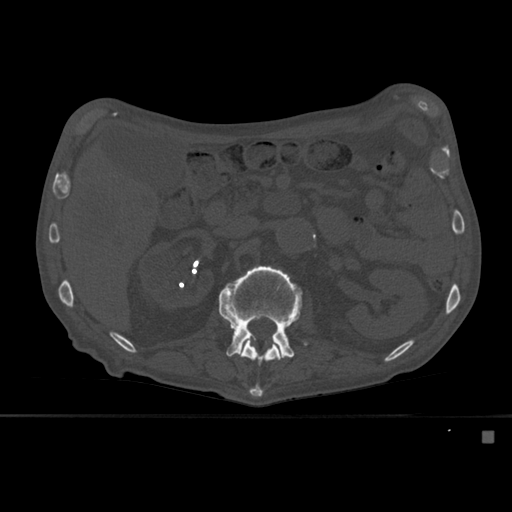
CT including the spine, one axial slice. Slice 243 of 527 in the series (ordered by position). Bone window (W 1800 / L 400 HU). 1.5 mm slice thickness. 512 × 512 image matrix, field of view 373 × 373 mm. Male patient, age 78 years. From the clinical record (not read from this slice): primary cancer: prostate.
Outlined on this slice (semi-automatically segmented with operator editing):
- L1 vertebra: bounding box <234,282,281,397> (left, top, right, bottom; pixels)
- L2 vertebra: <219,265,309,359>